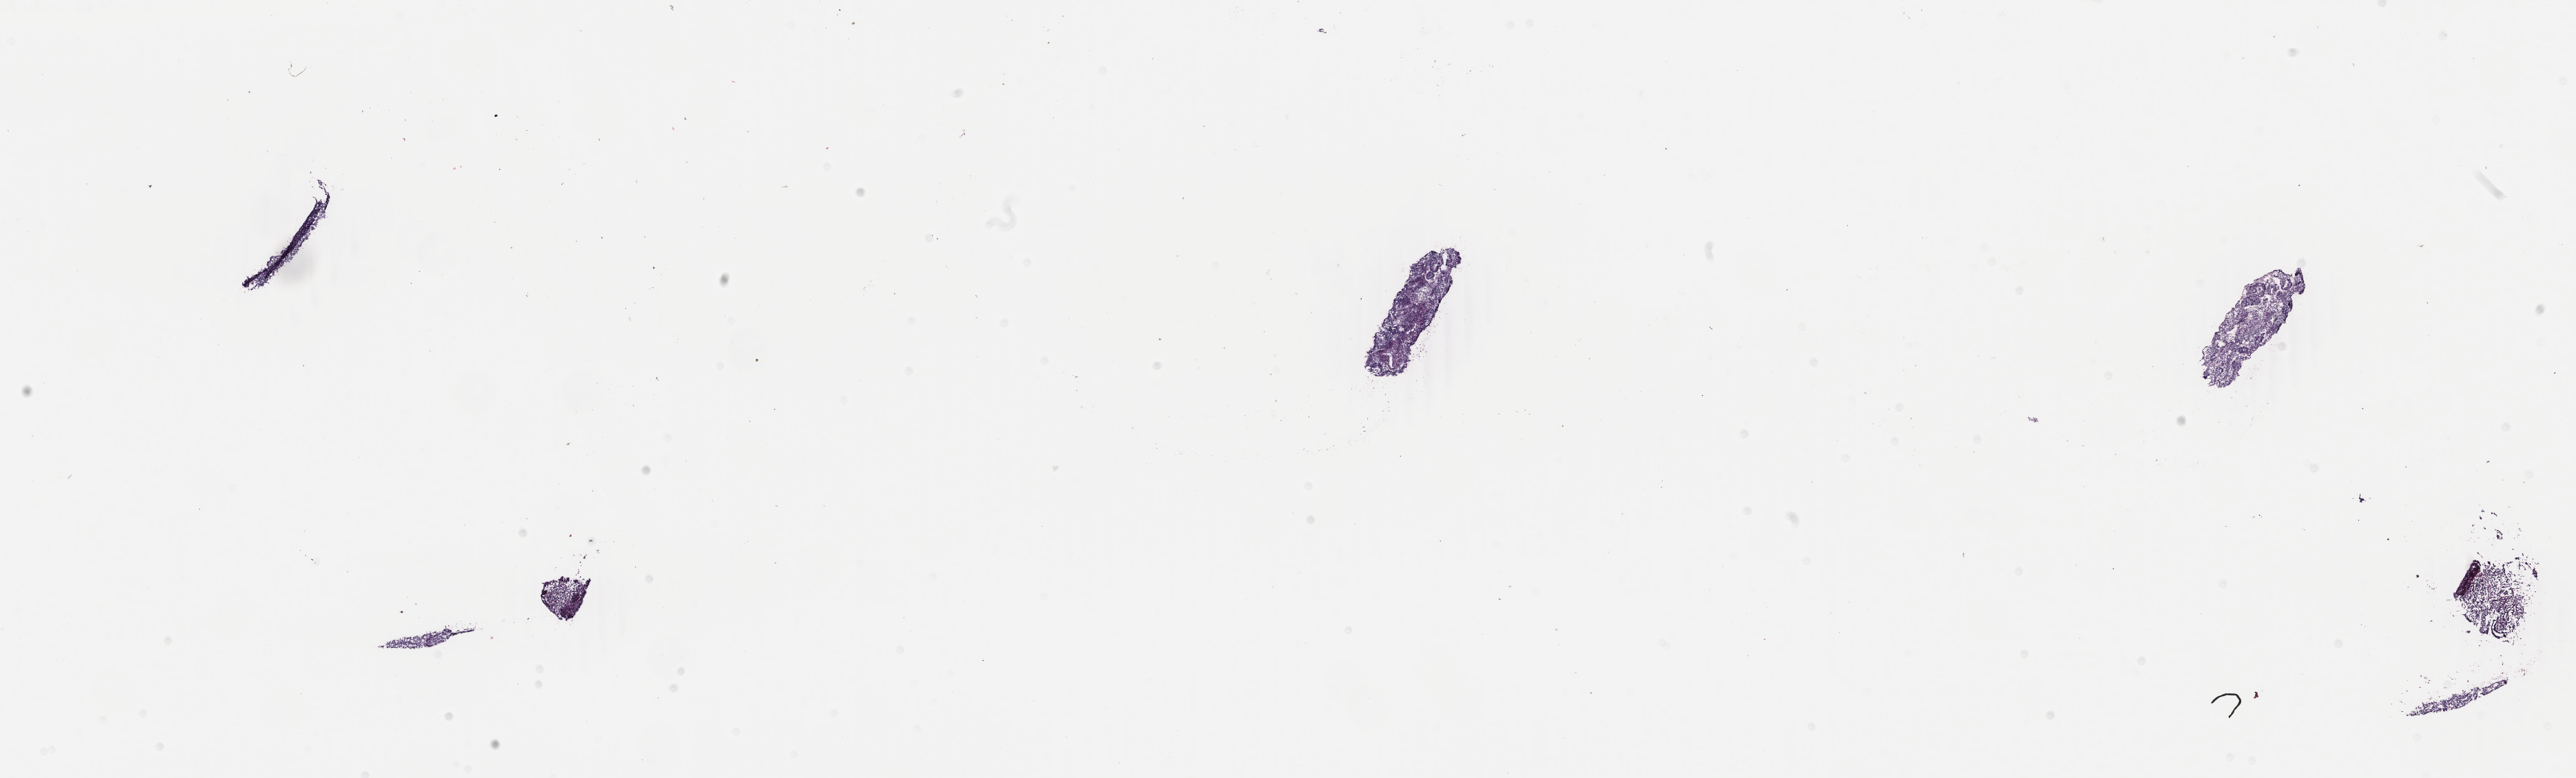
Whole-slide histology image, H&E, low-resolution overview of the scanned area, about 29.7 x 9.0 mm (acquisition: 40x scan); frozen section from the bottom of the tissue portion; sample: primary tumour, uterus. Female patient; age at initial diagnosis 53 years. Histologic grade: G1 (well differentiated). Slide review estimates, as recorded: tumour cells 60%, tumour nuclei 60%, normal cells 10%, stromal cells 30%, necrosis 0%. Inflammatory infiltration, as recorded: lymphocyte infiltration 40%, monocyte infiltration 40%, neutrophil infiltration 20%.
Histologic diagnosis: Endometrioid adenocarcinoma, NOS (endometrium). FIGO stage: IA.